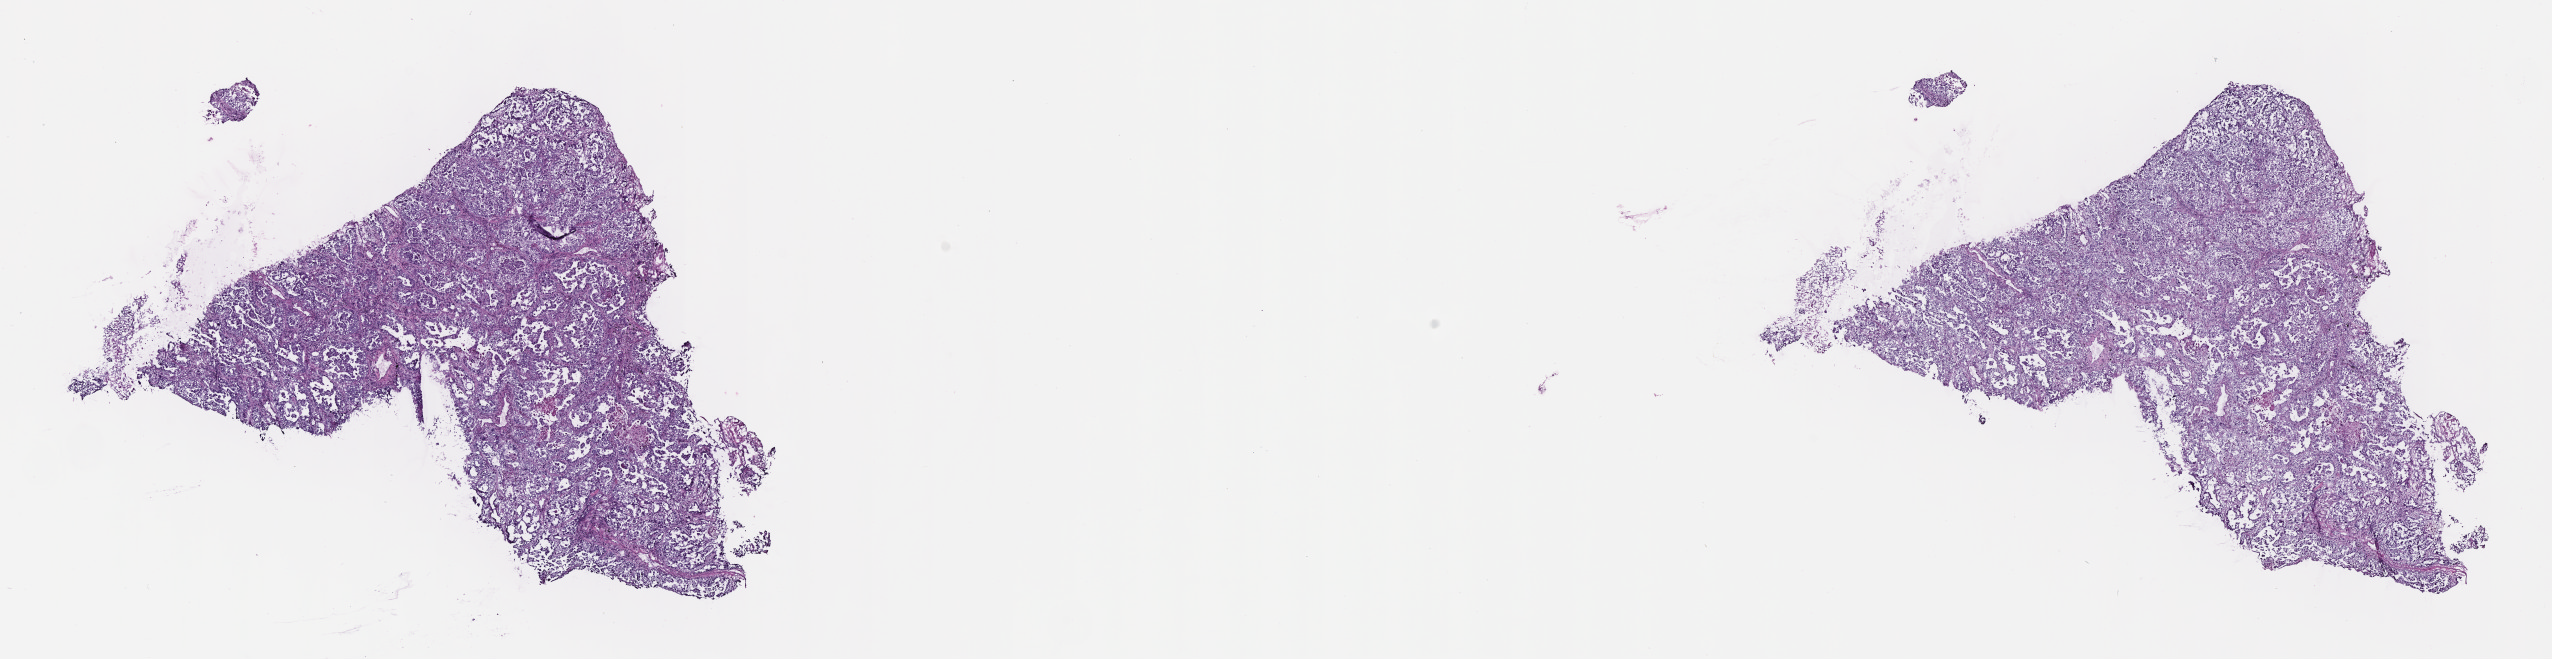
Whole-slide image, H&E stain — low-resolution overview of the scanned area, about 20.6 x 5.3 mm. Frozen section (tissue freezing medium). Specimen: primary tumor. Patient female; age 60 years. Slide review estimates, as recorded: tumor cells 75%, tumor nuclei 75%, stromal cells 23%, necrosis 2%, normal cells 0%. Inflammatory infiltration, as recorded: lymphocyte infiltration 3%, monocyte infiltration 3%, neutrophil infiltration 5%.
• diagnosis: Adenocarcinoma with mixed subtypes
• section: top of the tissue portion
• AJCC pathologic stage: Stage IIIA